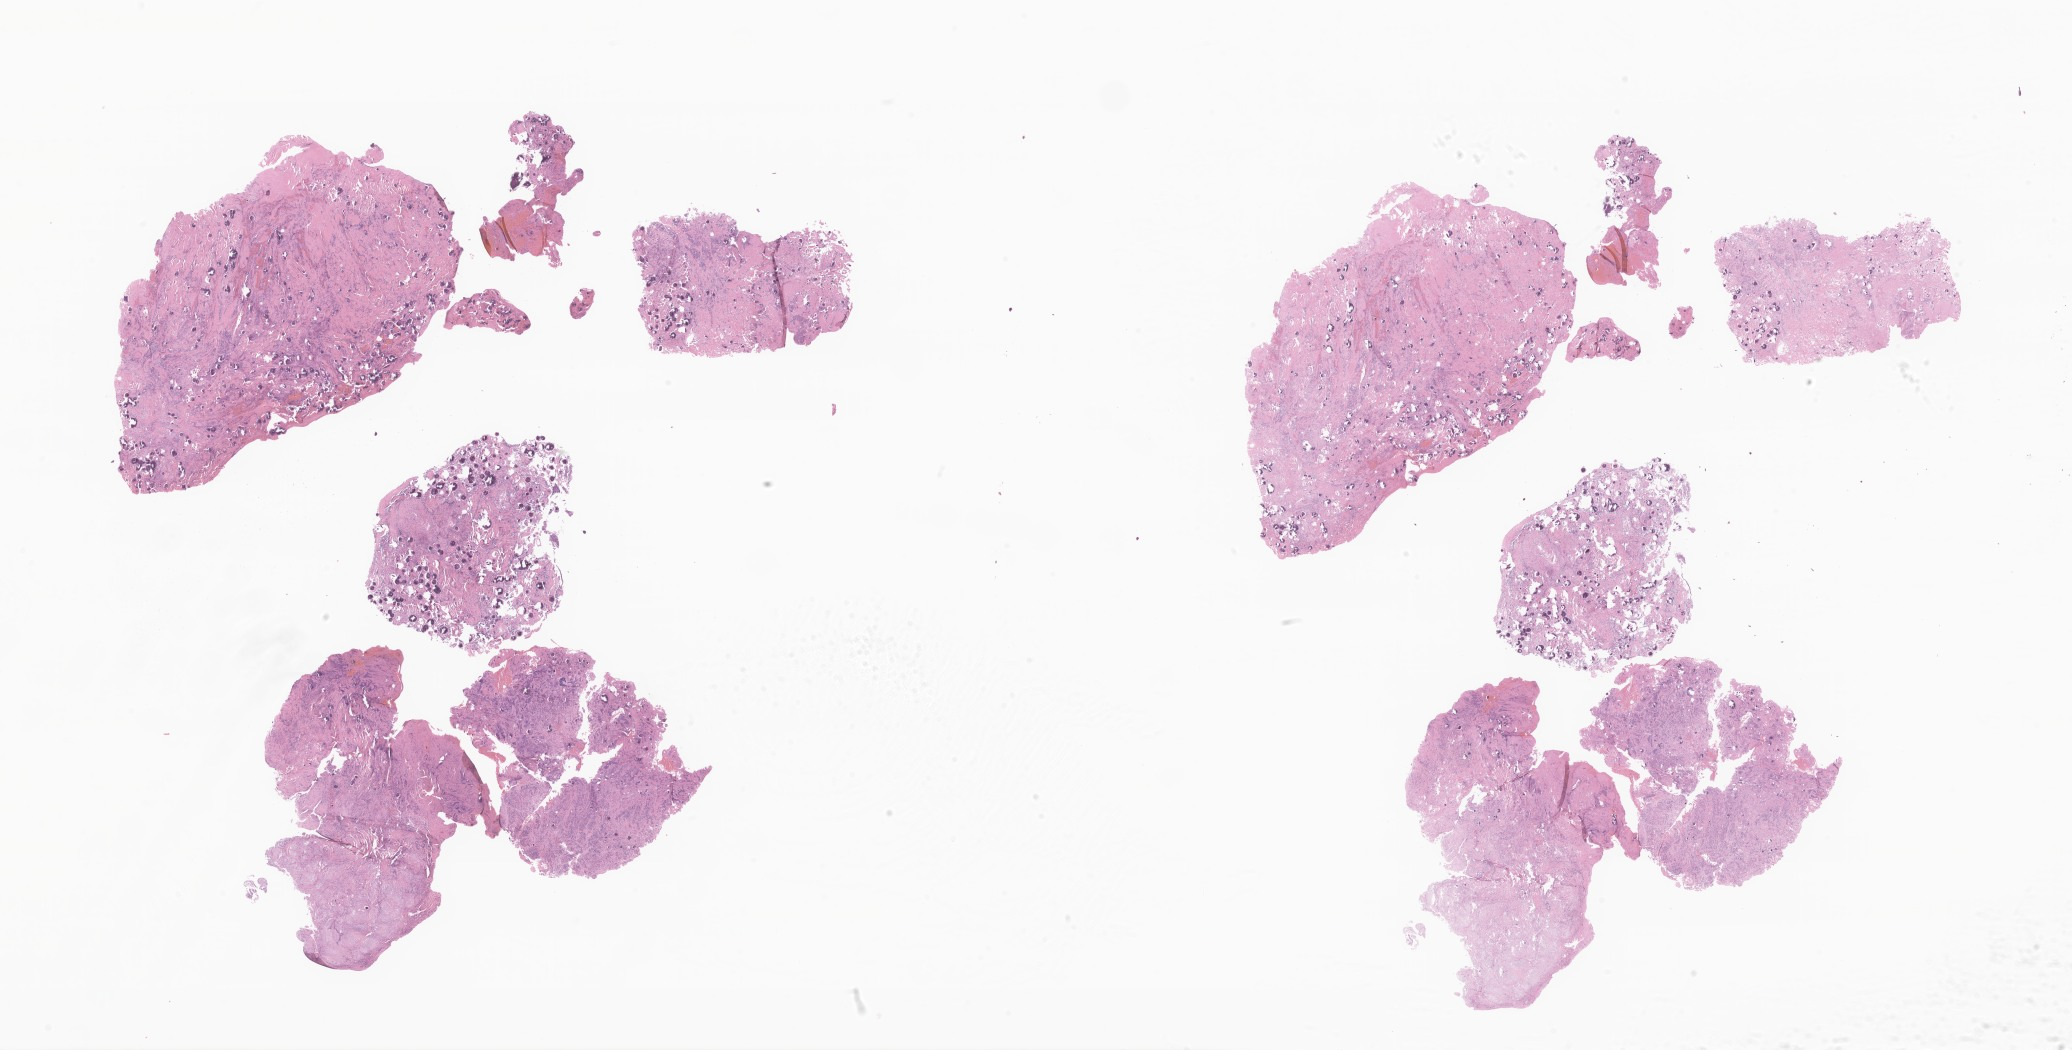
Whole-slide image, hematoxylin and eosin (H&E) stain of tumor tissue from the spinal cord — low-resolution overview of the scanned area, about 34.9 x 17.7 mm; formalin-fixed, paraffin-embedded (FFPE) tissue. Patient female; age 162 months (13 years 6 months).
* diagnosis: Meningioma, NOS